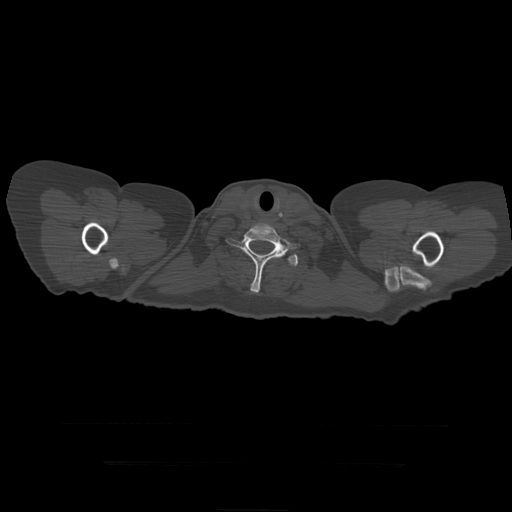
CT including the spine, one axial slice; slice 388 of 399 in the series (ordered by position); bone window (W 1800 / L 400 HU); 512 × 512 image matrix, field of view 450 × 450 mm. Patient age 41 years. From the clinical record (not read from this slice): primary cancer: breast.
Structures marked on this image (semi-automatic segmentation, software-assisted and operator-edited):
- T1 vertebra: bounding box [x1, y1, x2, y2] px = [226, 223, 300, 293]
- T2 vertebra: [288, 257, 299, 267]